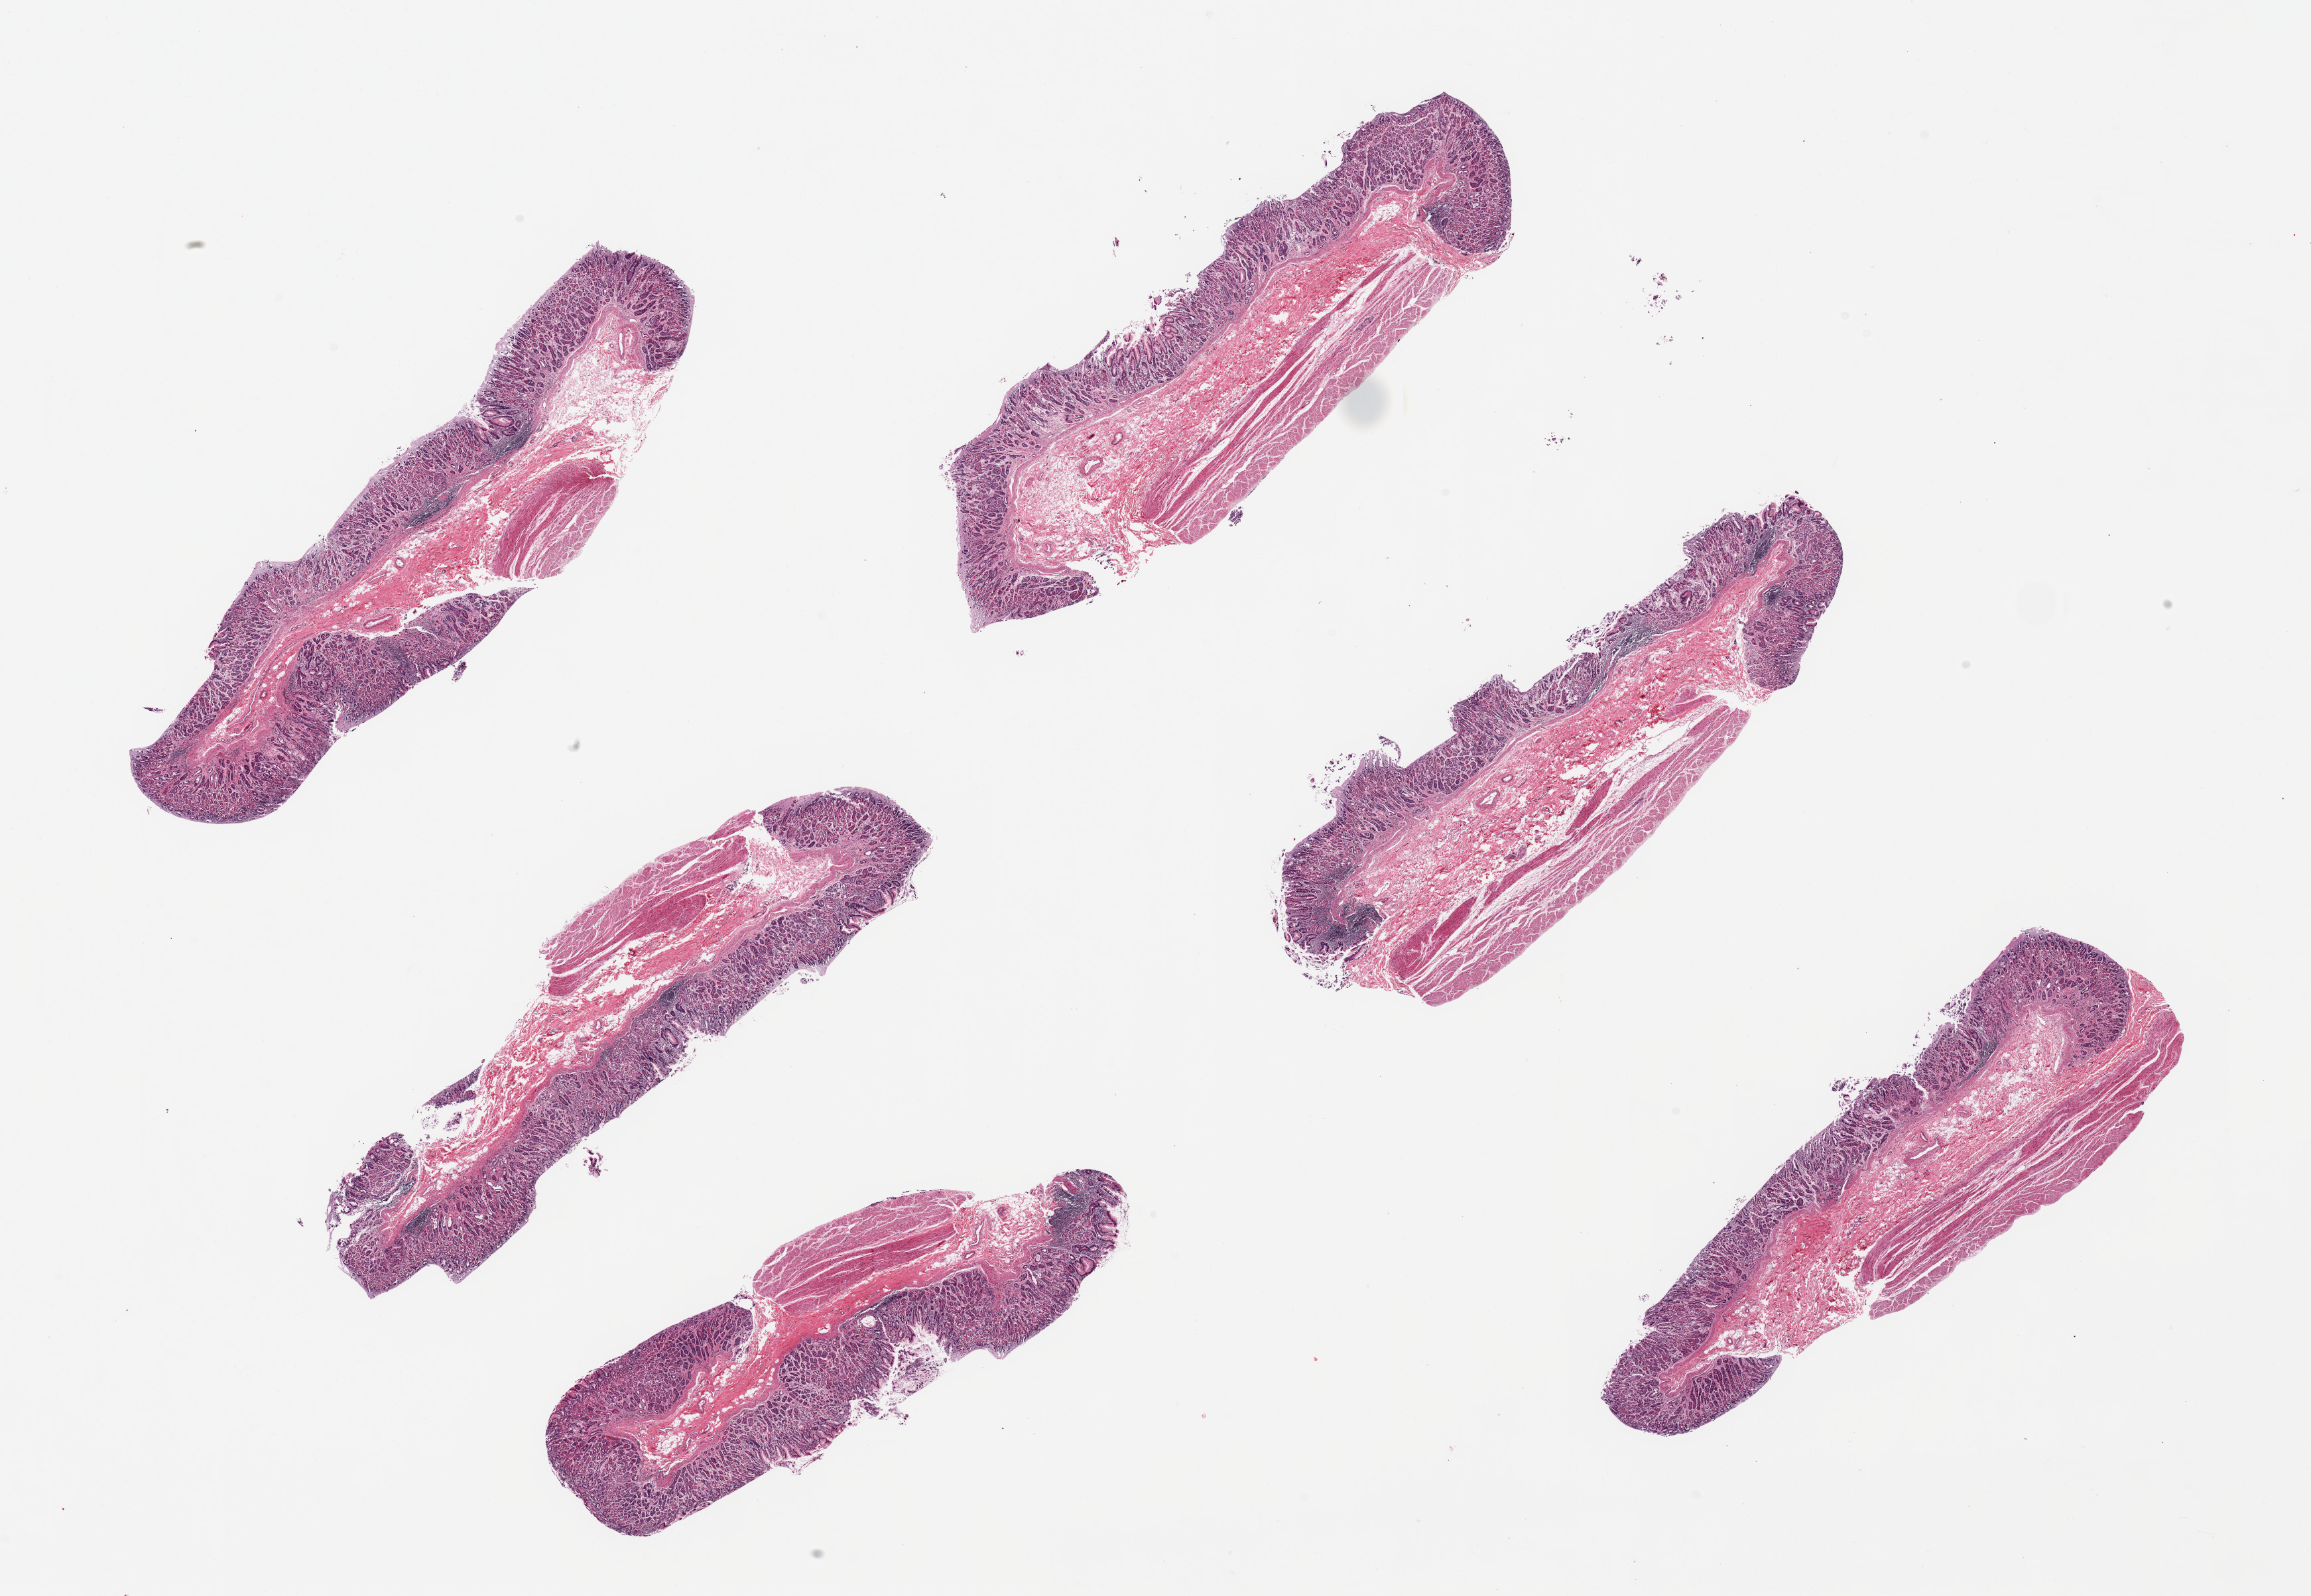
Digitized H&E-stained section — whole scanned area (about 27.6 x 19.0 mm) shown as a low-resolution overview, PAXgene-fixed, paraffin-embedded tissue, sampled site (target tissue): stomach, donor tissue sample. Donor: female.
Pathologist's review note for this sample: 6 pieces ~8.5x2mm. Slight to focally moderate chronic gastritis.